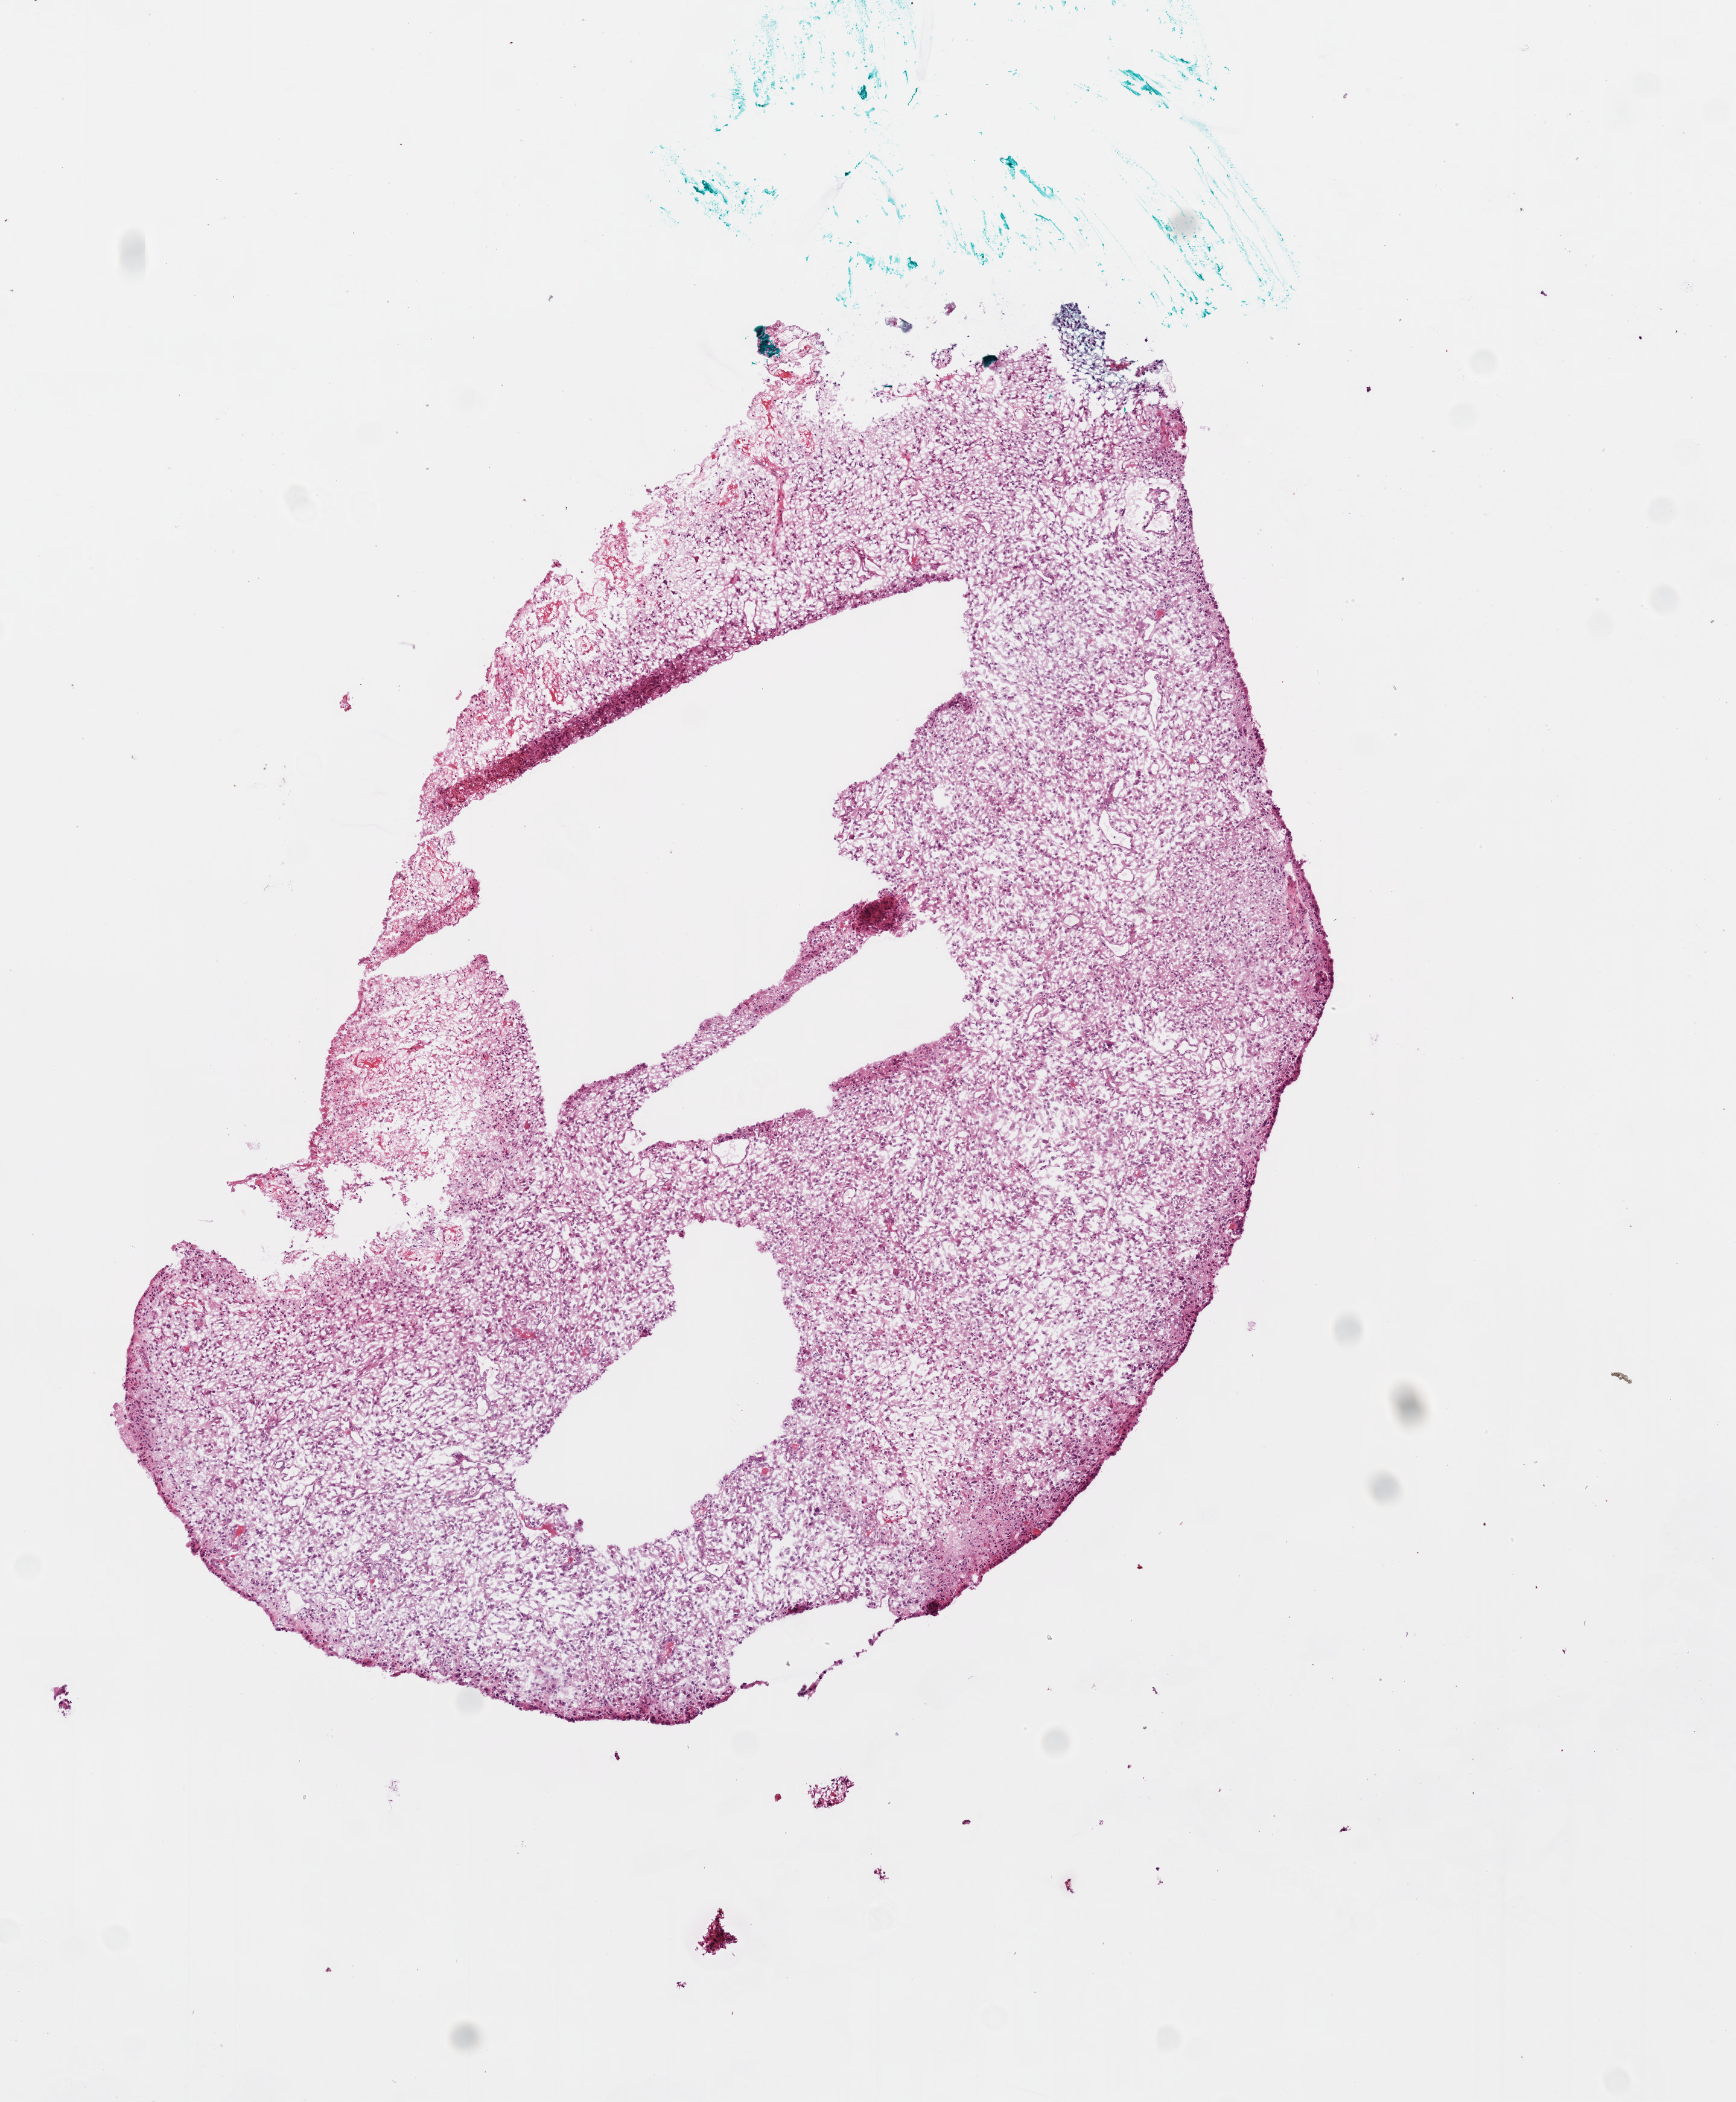
Whole-slide histology image, Hematoxylin and eosin (H&E) stained — shown as a low-resolution overview of the whole scanned area (about 5.8 x 7.0 mm), frozen section from the bottom of the tissue portion, sample: primary tumour, brain. Patient: male, age at initial diagnosis 53 years. Composition of this section per pathologist review: tumour cells 80%, tumour nuclei 100%, normal cells 0%, stromal cells 0%, necrosis 20%.
• diagnosis: Glioblastoma